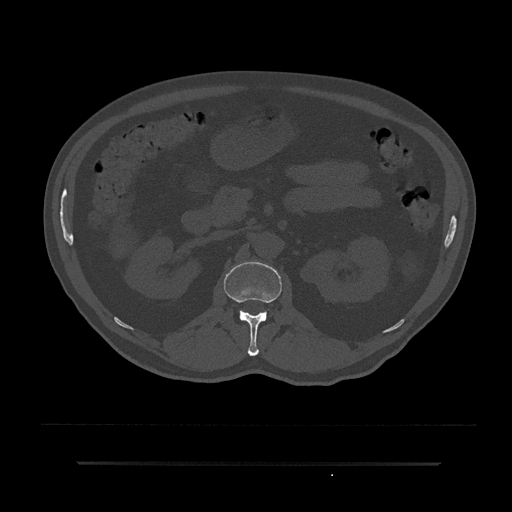
CT including the spine, one axial slice. Position 130 of 797 along the scan axis. Reconstruction kernel Br40s/3. 120 kVp. Bone window (W 1800 / L 400 HU). 0.5 mm slice thickness. 512 × 512 image matrix, field of view 464 × 464 mm. Patient: male, 59 years. From the clinical record (not read from this slice): primary cancer: bile ducts; vertebrae with lytic lesions (as recorded): T10.
Outlined on this slice (semi-automatic segmentation, software-assisted and operator-edited):
- L1 vertebra: bounding box <224,262,282,356> (left, top, right, bottom; pixels)